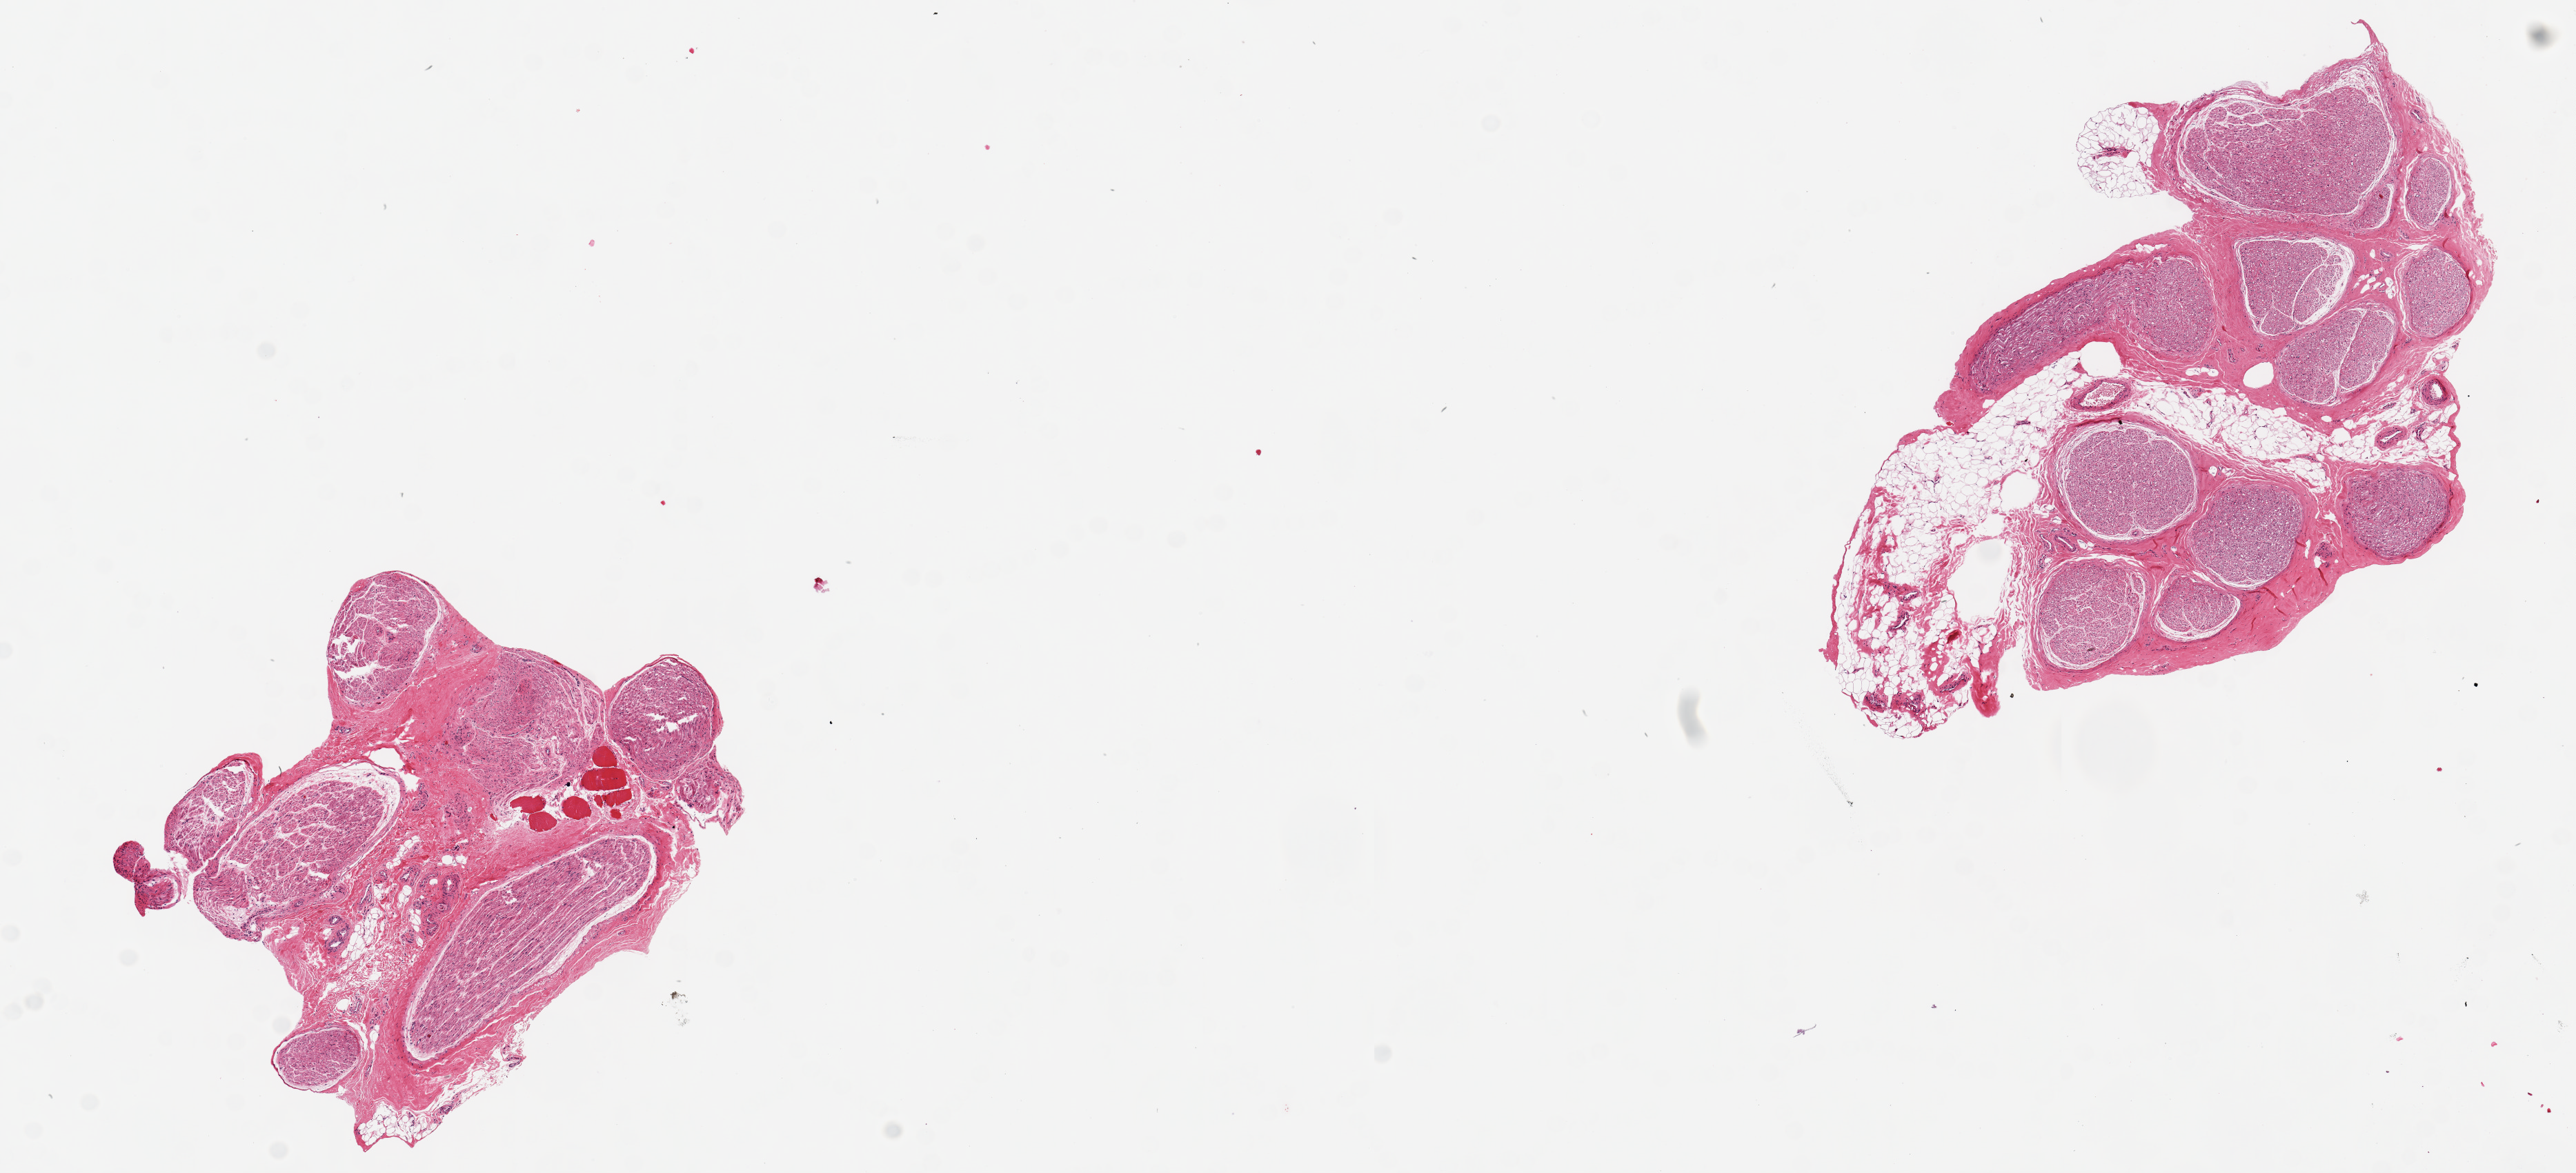
Whole-slide image, H&E stain, brightfield, low-resolution overview of the scanned area, about 14.8 x 6.7 mm (from a 20x scan). PAXgene-fixed paraffin-embedded (PFPE) section. Section of tibial nerve (target tissue). Donor tissue sample. Male donor.
Reviewer comment on this tissue sample: 2 pieces, 5x4 & 3x2.5mm; ~30% adipose in 1 piece.